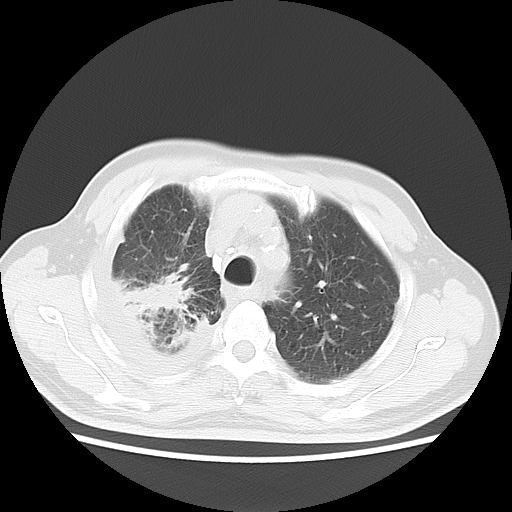
Chest CT, one axial slice; slice 12 of 16 in the series (ordered by position); reconstruction kernel LUNG; lung window (W 1500 / L -600 HU); 512 × 512 image matrix, field of view 350 × 350 mm. Patient: male, 75 years. Case-level facts recorded for this patient, not image findings: clinical TNM (as recorded): T1c N1 M1.
Structures marked on this image (bounding box drawn by a radiologist):
- lung tumour (recorded histology: adenocarcinoma): box from (x=117, y=272) to (x=198, y=318) px